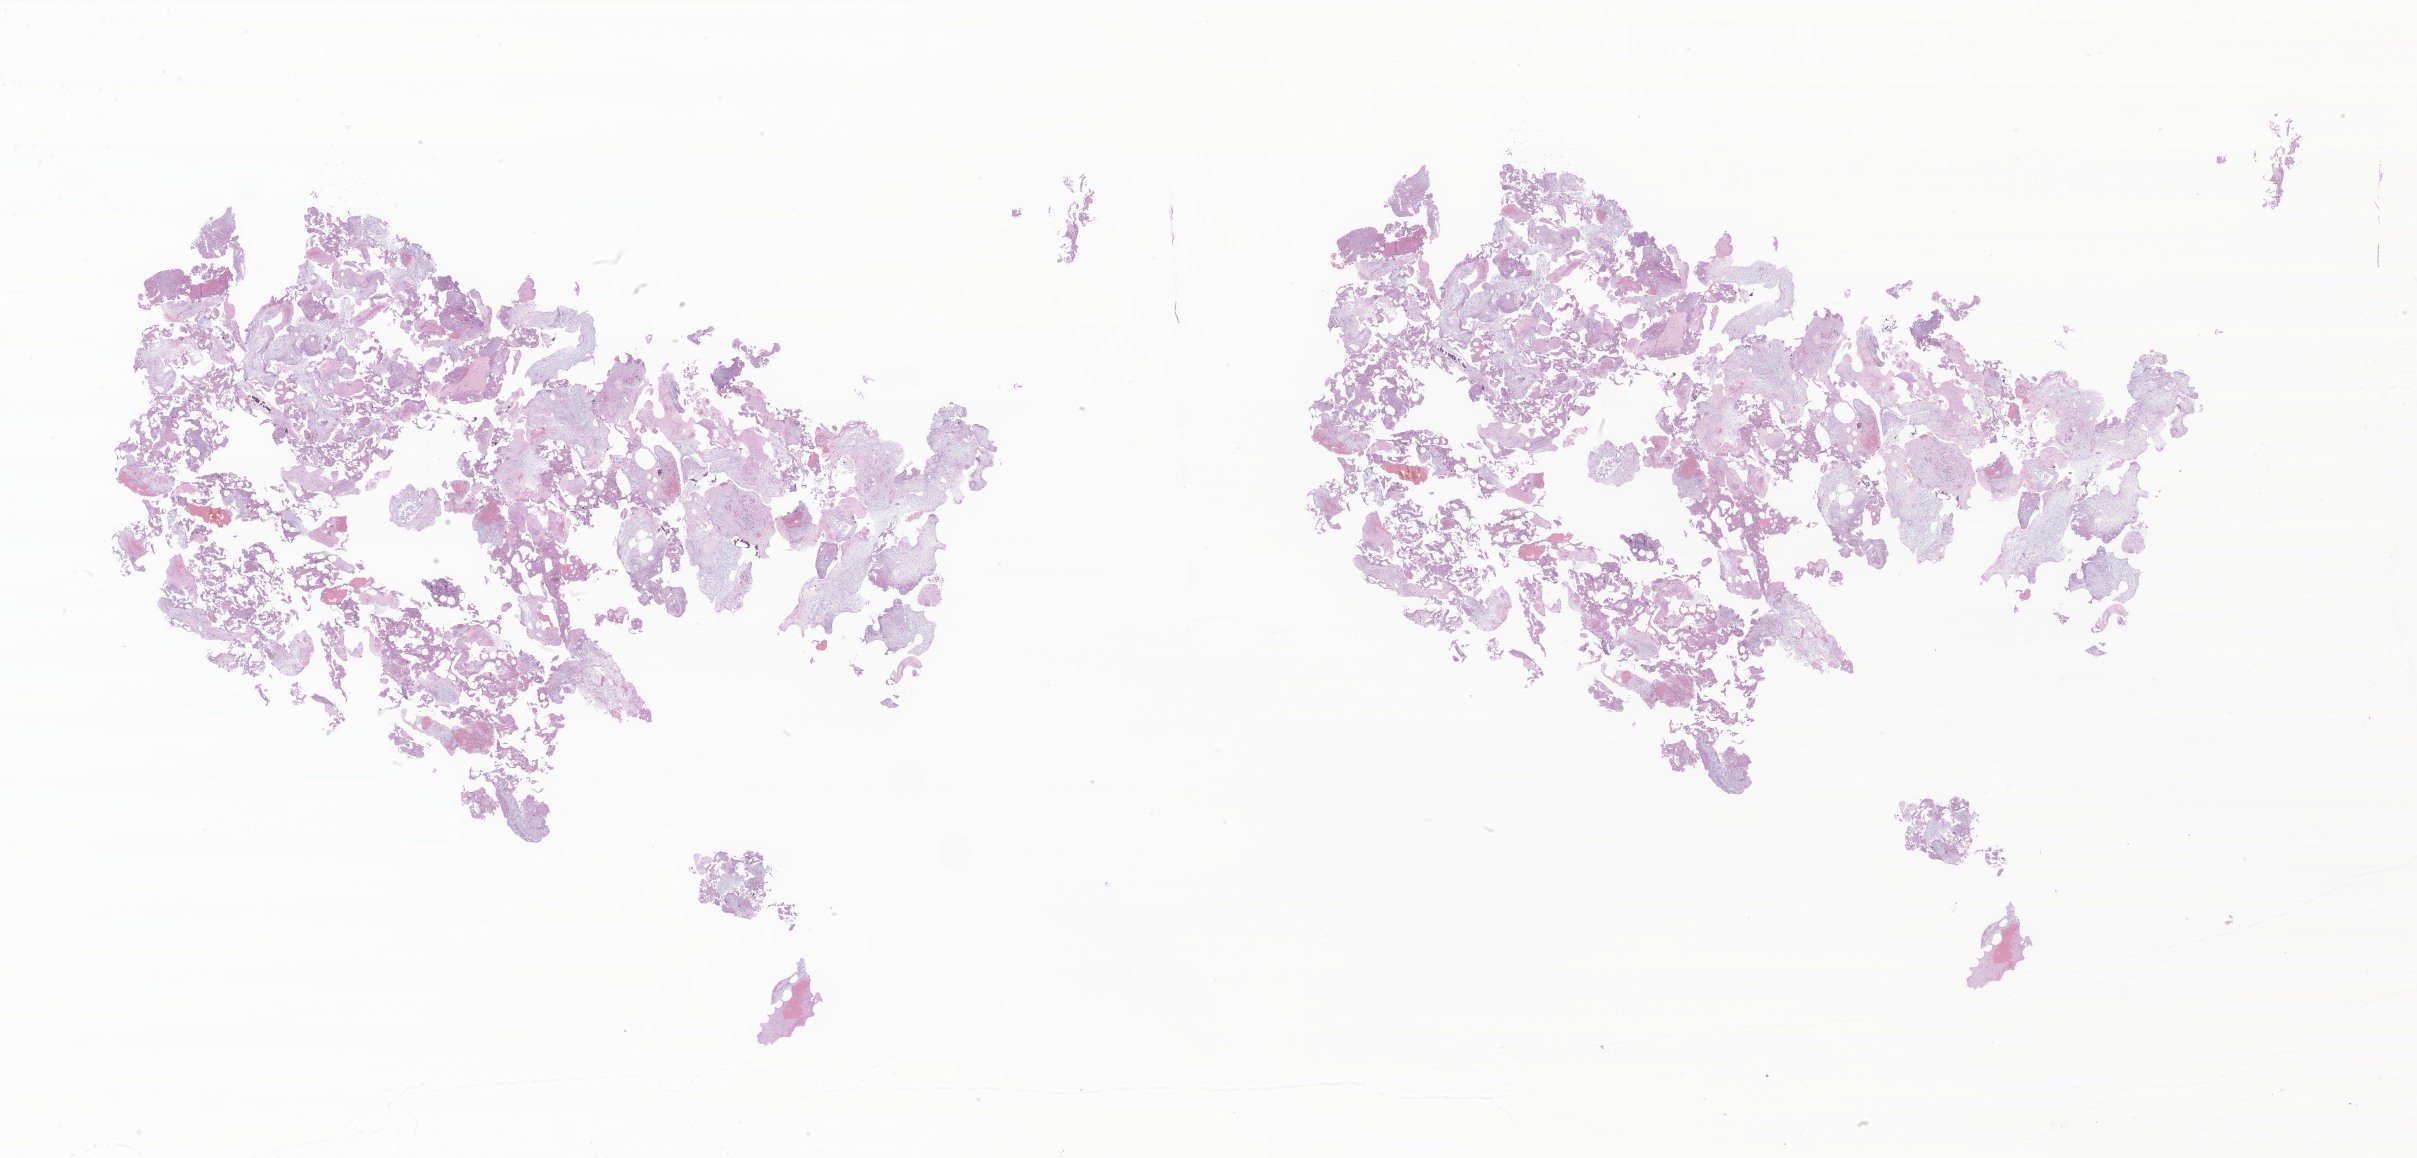
H&E whole-slide image of tumor tissue from the brain, low-resolution overview of the scanned area, about 40.8 x 19.5 mm, FFPE section. Patient female; age 102 months.
Diagnosis (ICD-O-3 morphology term): Mixed germ cell tumor.